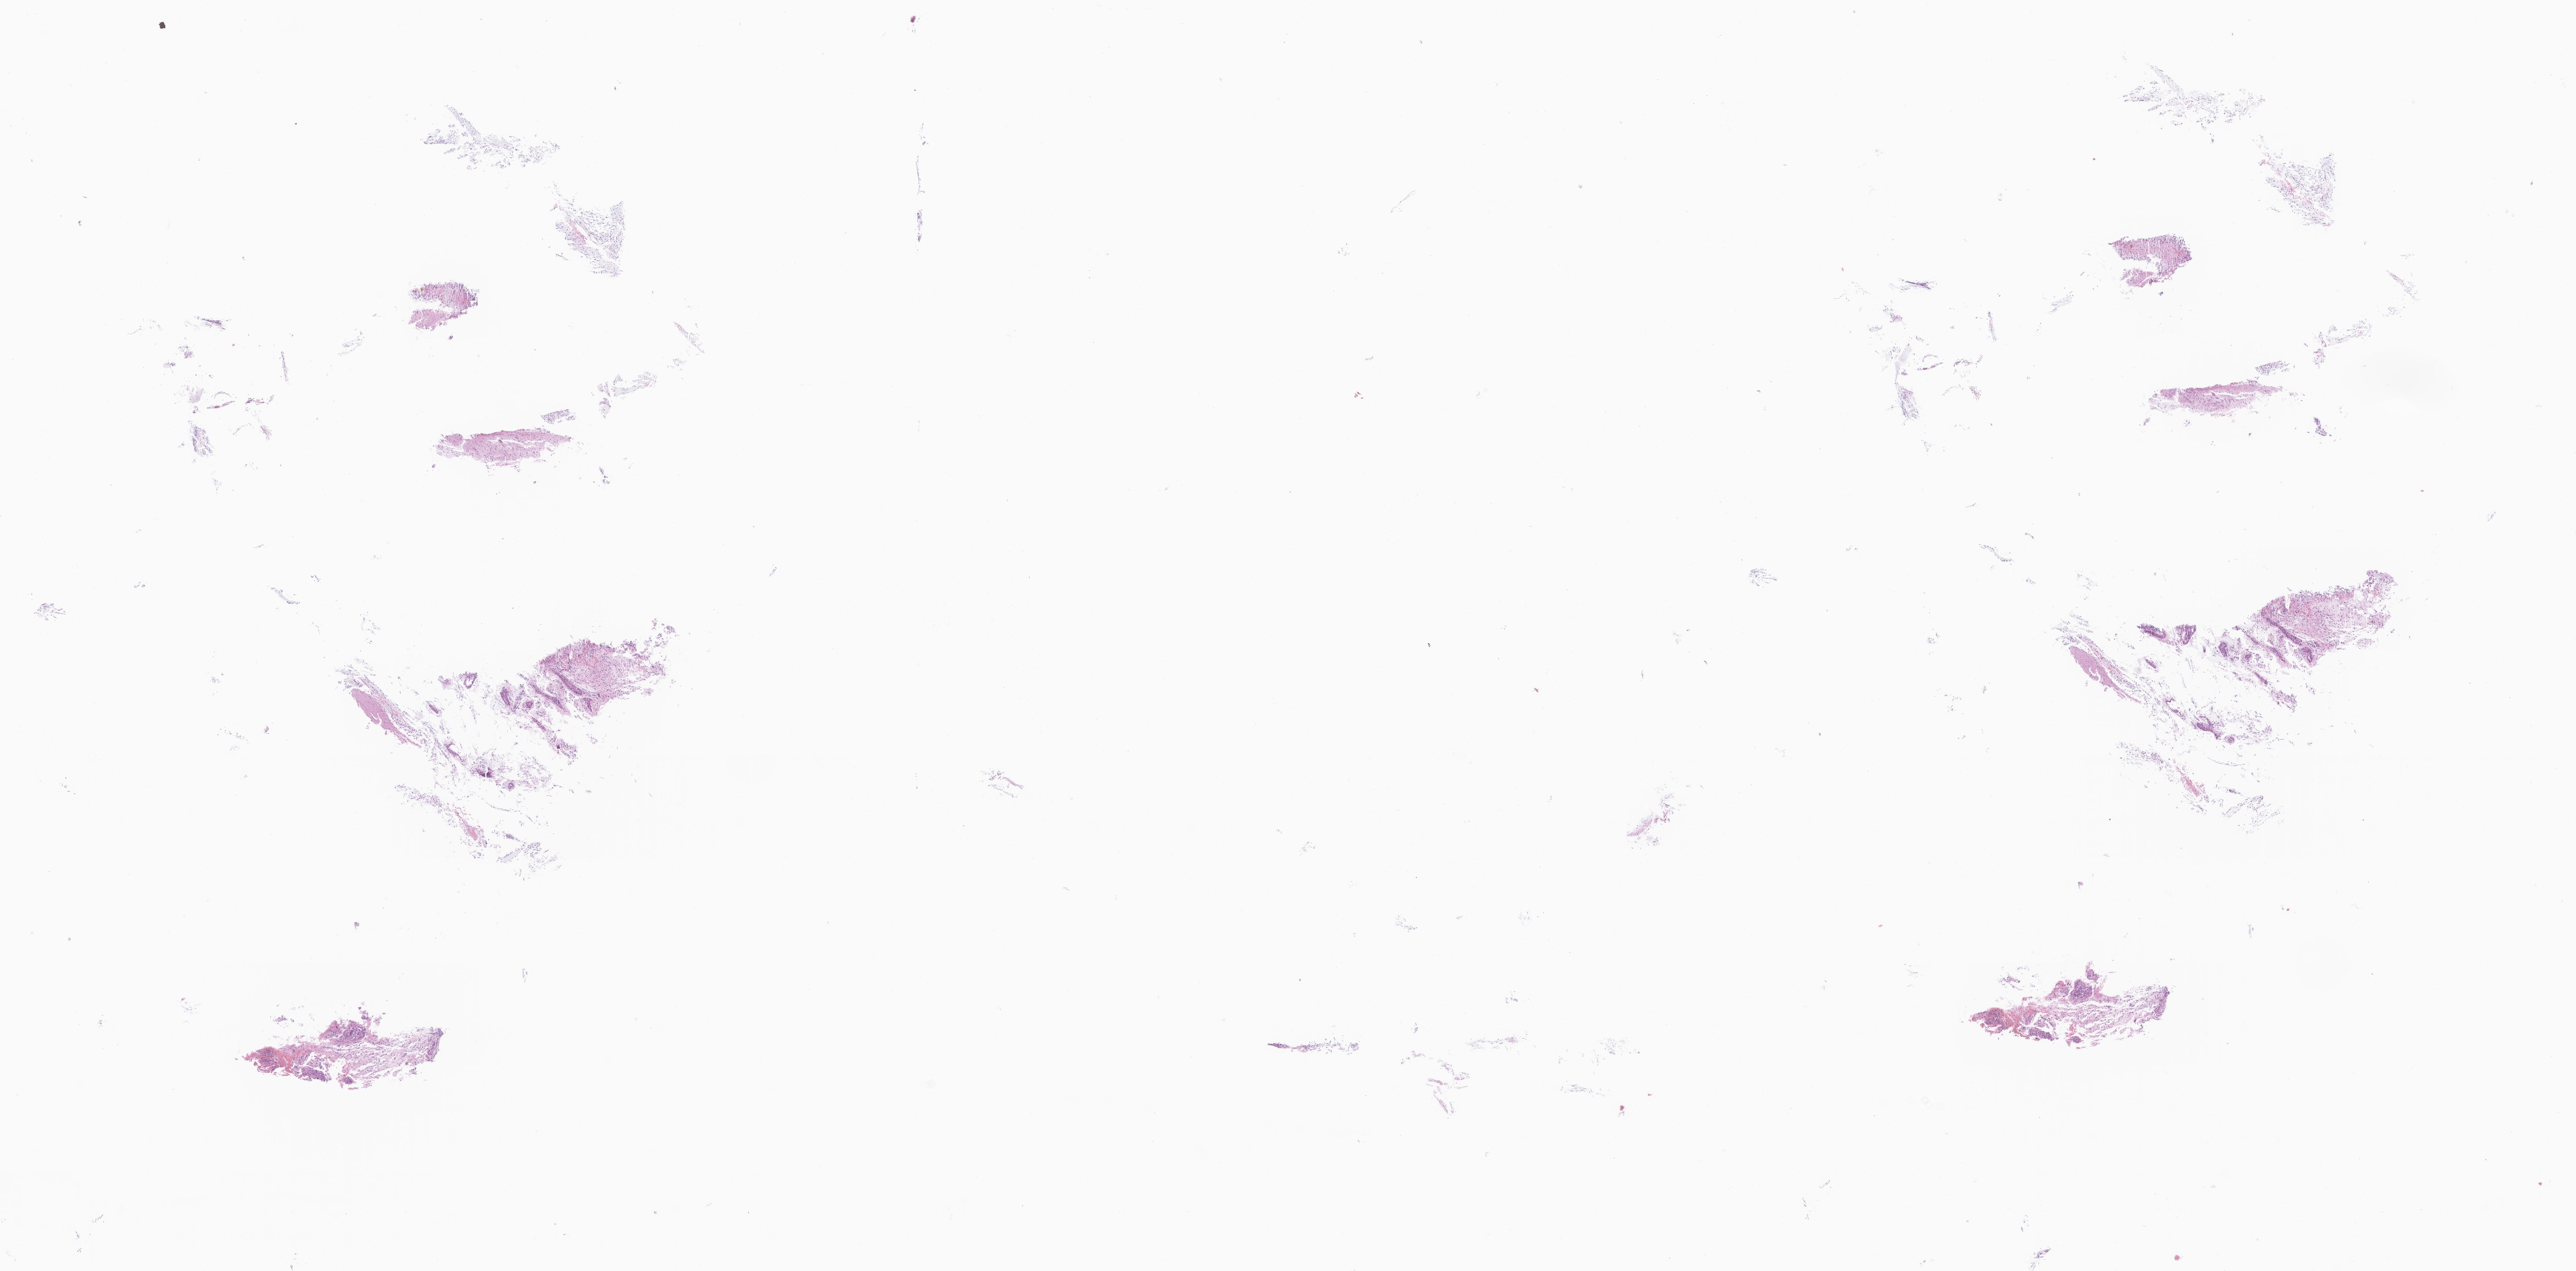
Digitized H&E-stained section of tumor tissue from the brain, whole scanned area (about 26.5 x 13.1 mm) shown as a low-resolution overview; formalin-fixed paraffin-embedded section. Patient: male, age 169 months (14 years 1 month).
* diagnosis (ICD-O-3 morphology term): Astrocytoma, NOS